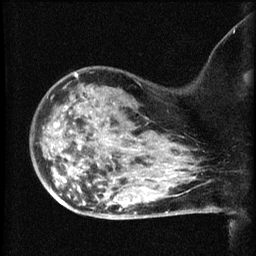
Breast MRI (dynamic contrast-enhanced), one sagittal slice; dynamic contrast-enhanced series, image 2 of 3 at this slice position (ordered by acquisition); 1.5 T; TE 4.2 ms, TR 8.2 ms; 2.1 mm slice thickness; 256 × 256 image matrix. Female patient, age 50 years.
Structures marked on this image (semi-automatic segmentation, software-assisted and operator-edited):
- analysis volume of interest (the breast-tissue region the enhancement analysis was run in; not a lesion): bounding box [x1, y1, x2, y2] px = [38, 77, 169, 211]
- tumour enhancement mask (voxels above the 70 % enhancement threshold inside the analysis volume of interest): [60, 201, 64, 204]